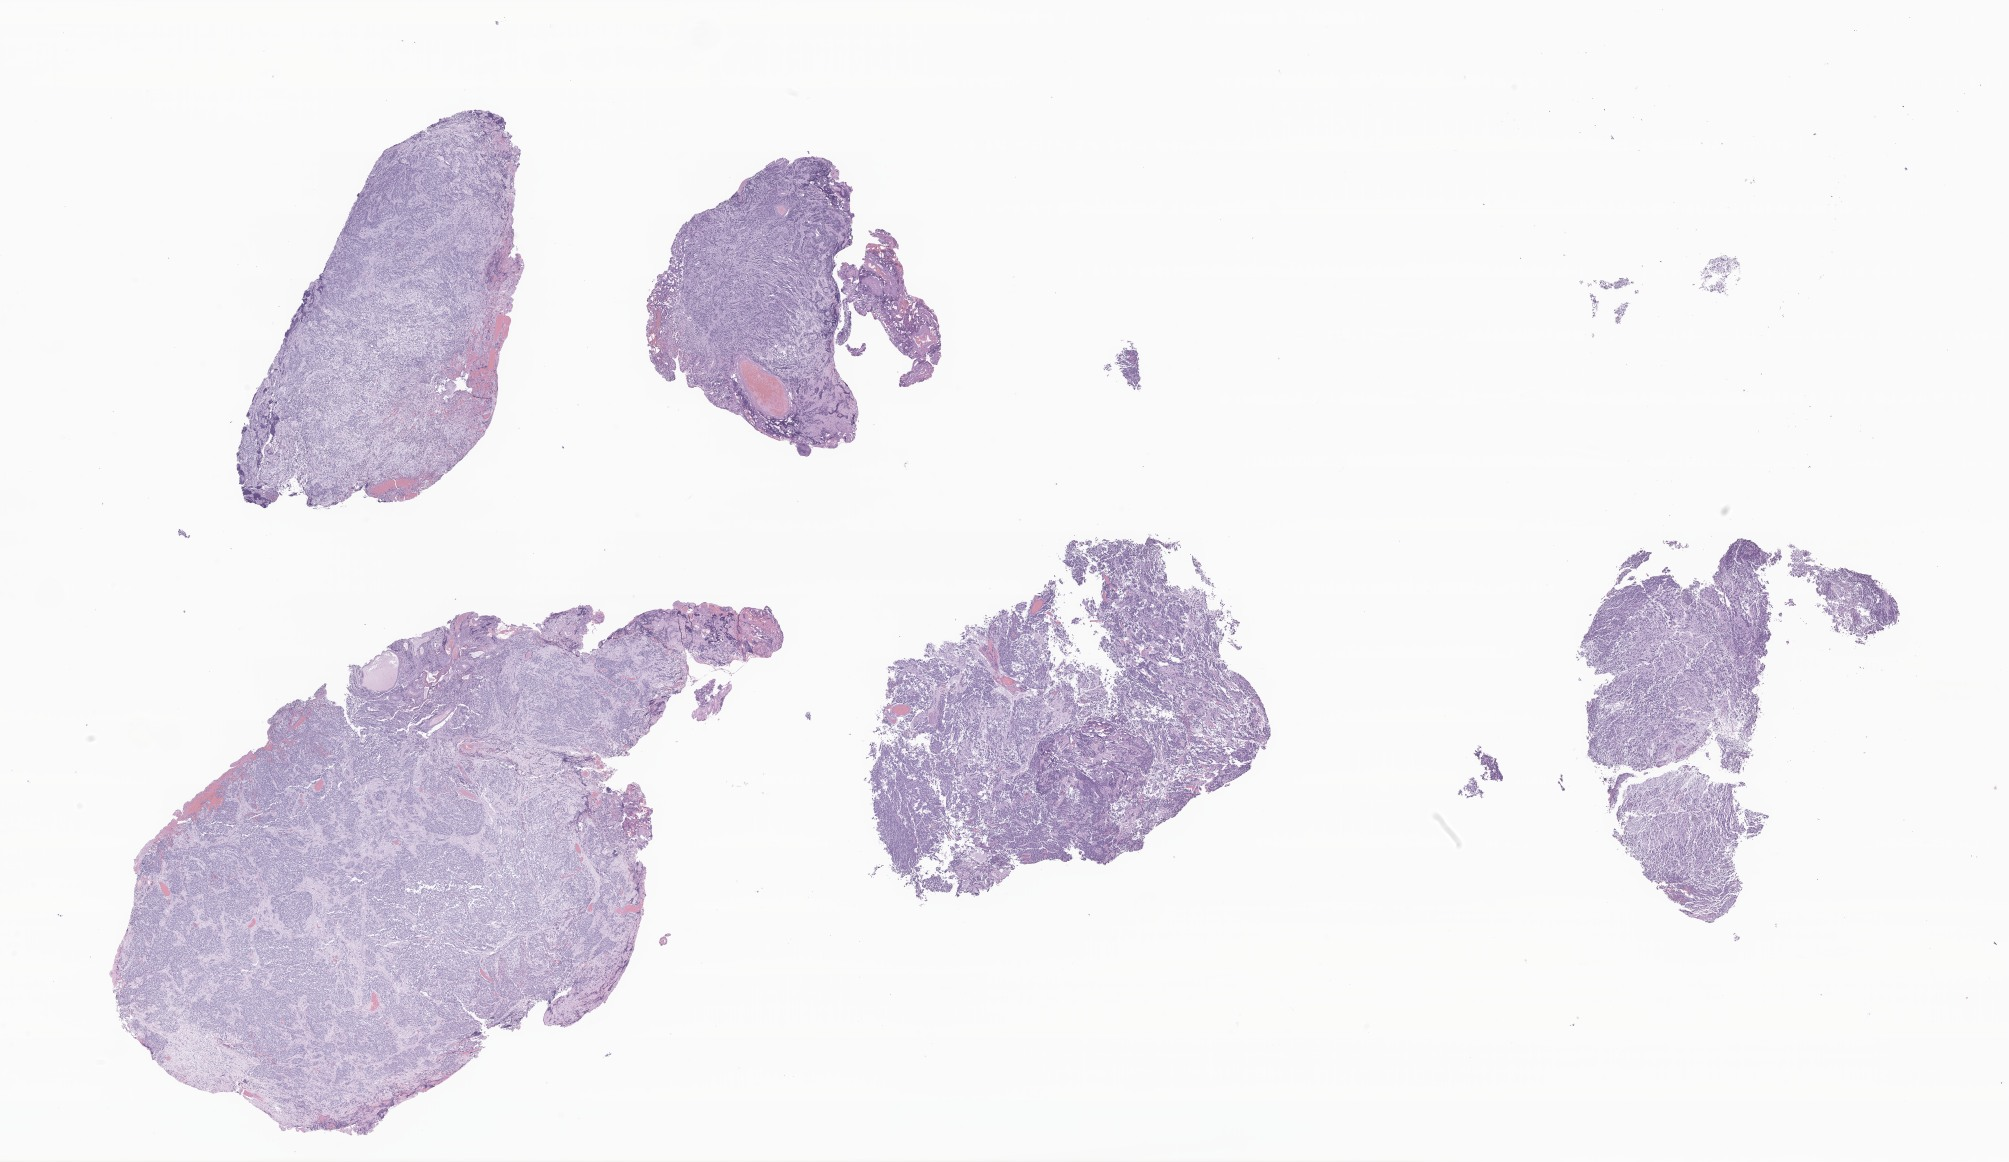
Whole-slide image, haematoxylin and eosin stain of tumor tissue from the brain, a low-resolution overview of the entire scanned area, about 33.9 x 19.6 mm, formalin-fixed paraffin-embedded section. Patient female; age 68 months (5 years 8 months).
Diagnosis: Medulloblastoma, NOS.